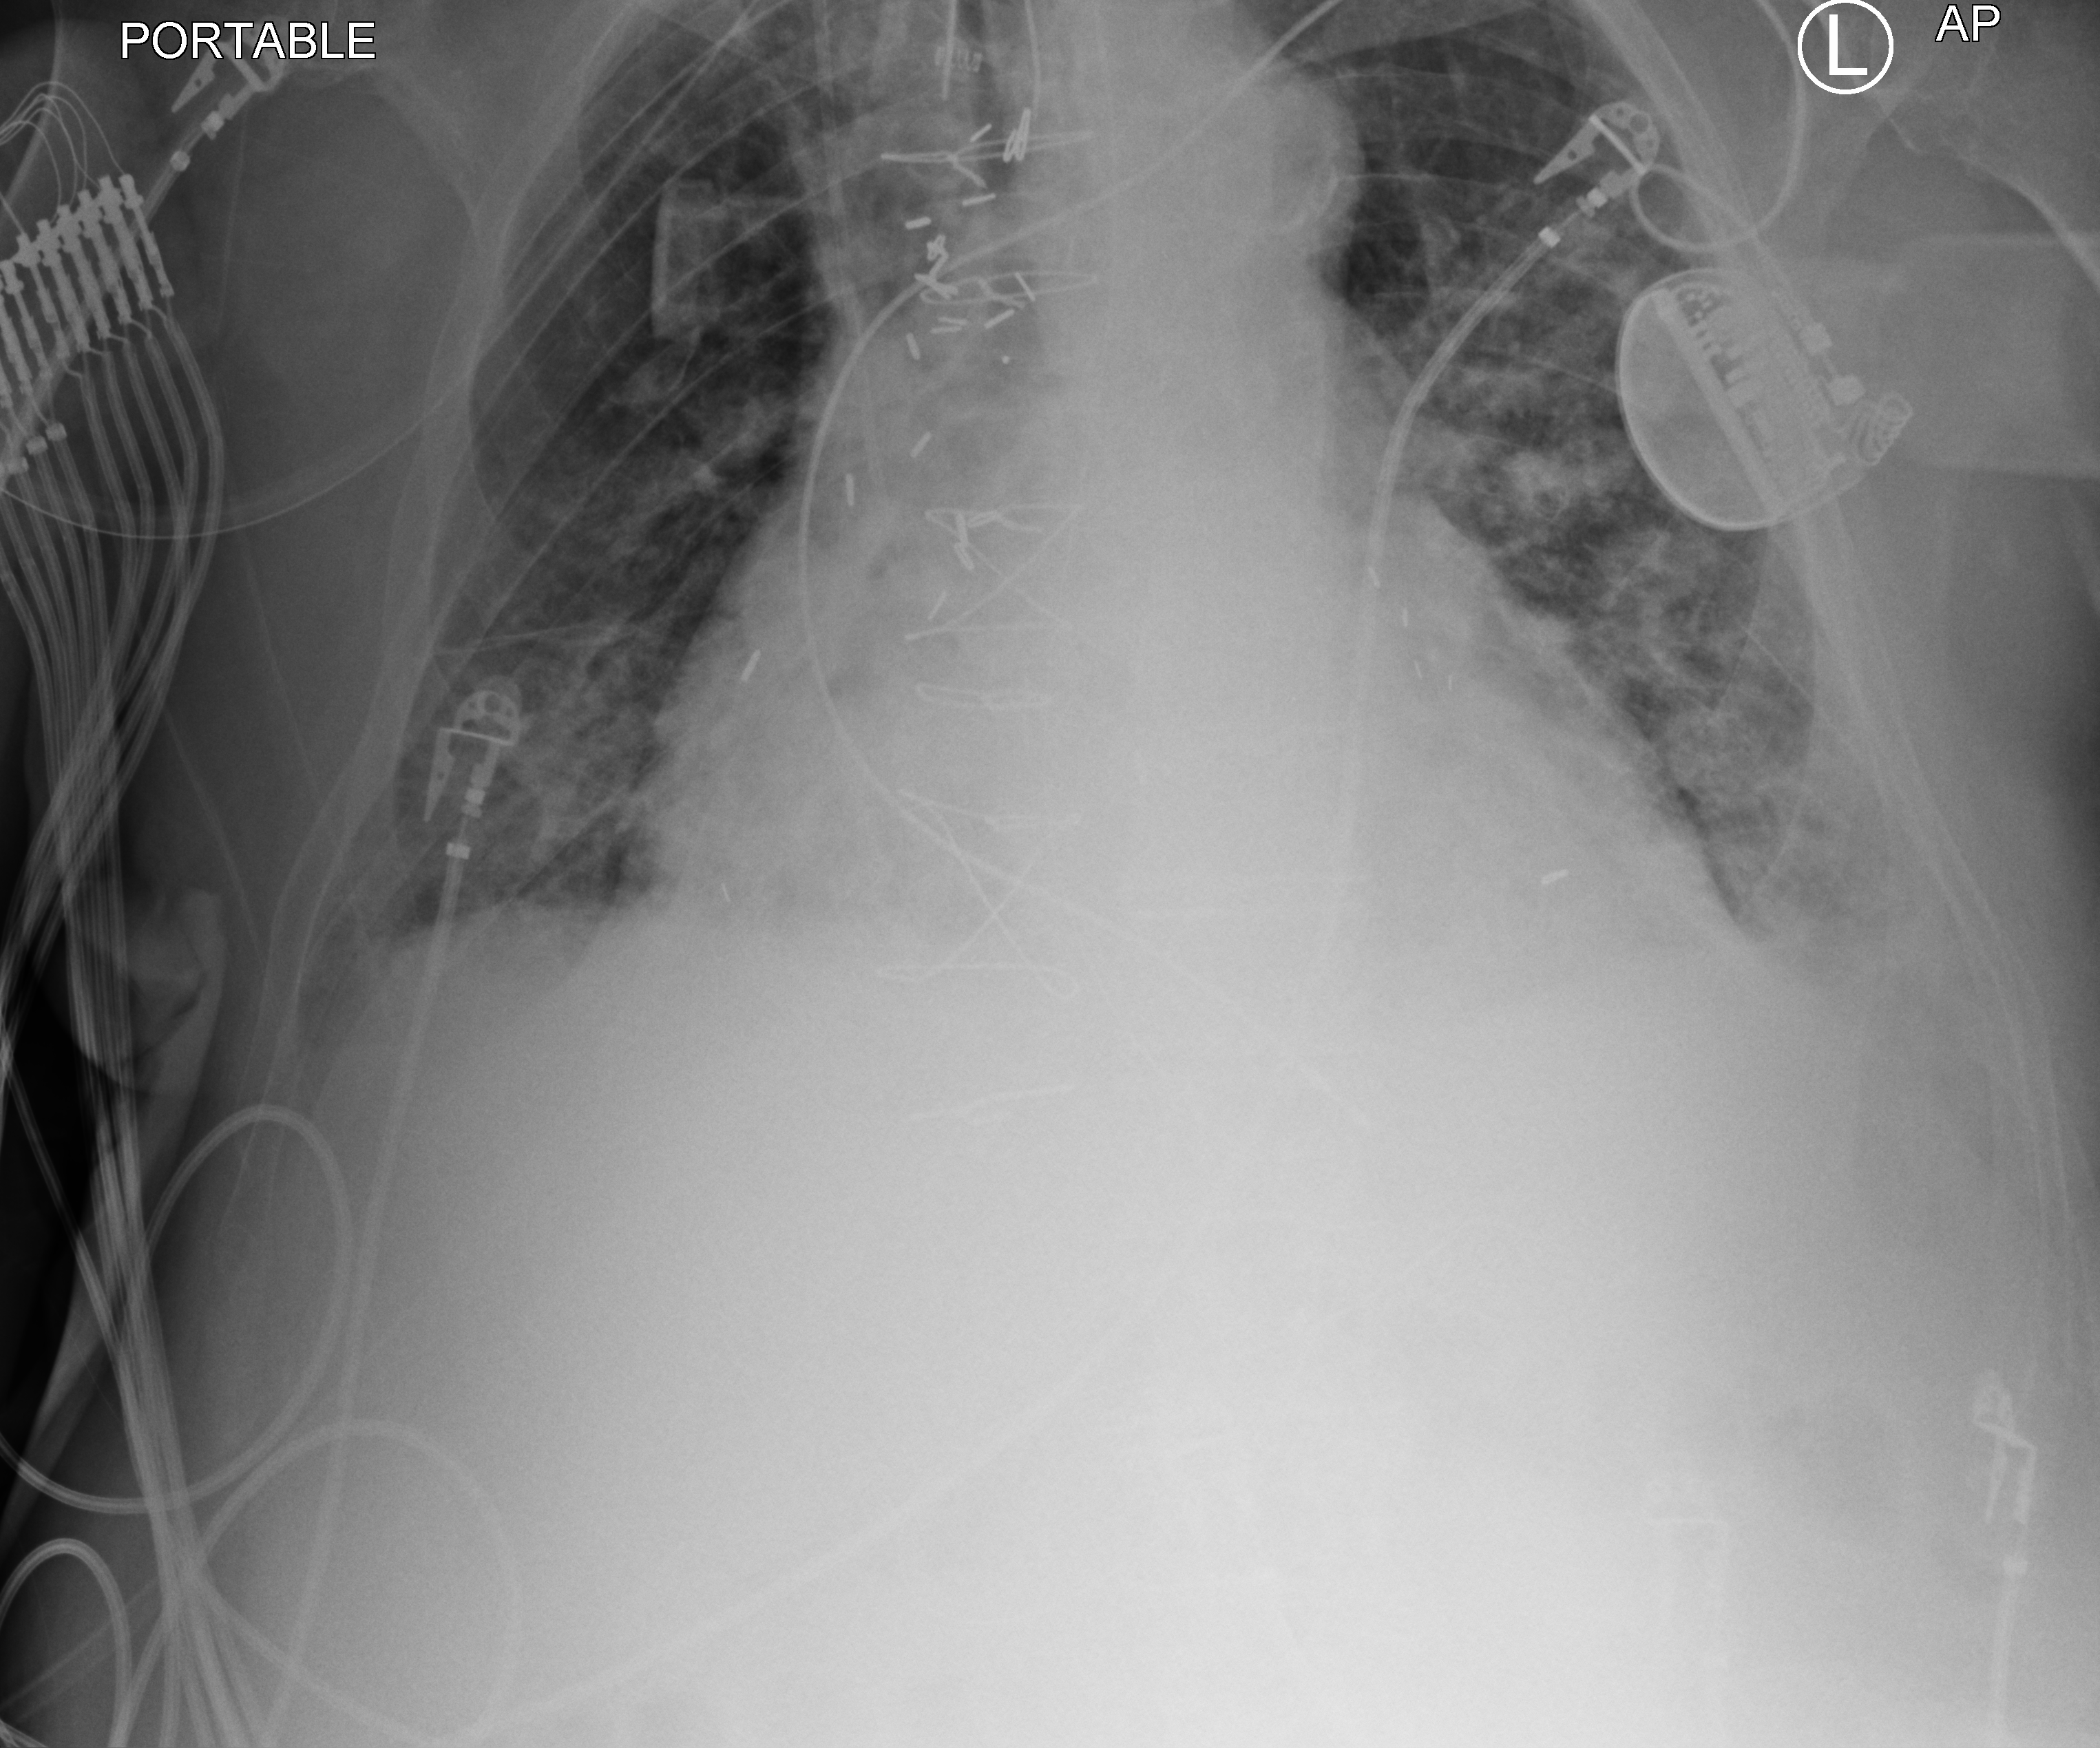
Chest X-ray (portable). Male patient hospitalised with COVID-19, age 75–90 years.
From the hospital-stay record, not from the radiograph (when in the stay this image was taken is not recorded): length of hospital stay: 16 days; diabetes (admission record): yes.